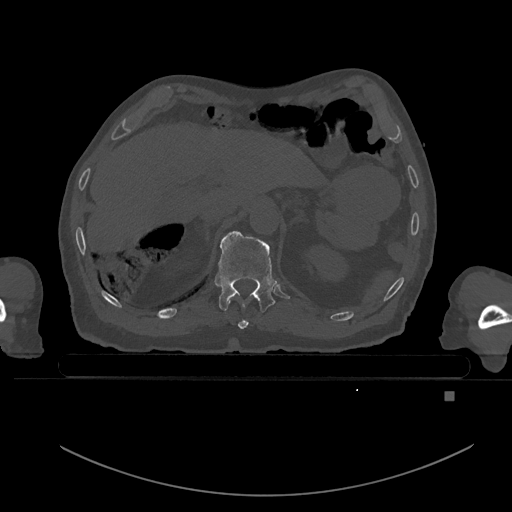
CT including the spine, one axial slice. Position 42 of 969 along the scan axis. Bone window (W 1800 / L 400 HU). 512 × 512 image matrix, field of view 456 × 456 mm. Male patient, age 82 years. Case-level facts recorded for this patient, not image findings: primary cancer: prostate.
Outlined on this slice (semi-automatic segmentation, software-assisted and operator-edited):
- T10 vertebra: bounding box [x1, y1, x2, y2] px = [238, 320, 248, 329]
- T11 vertebra: [215, 230, 278, 313]